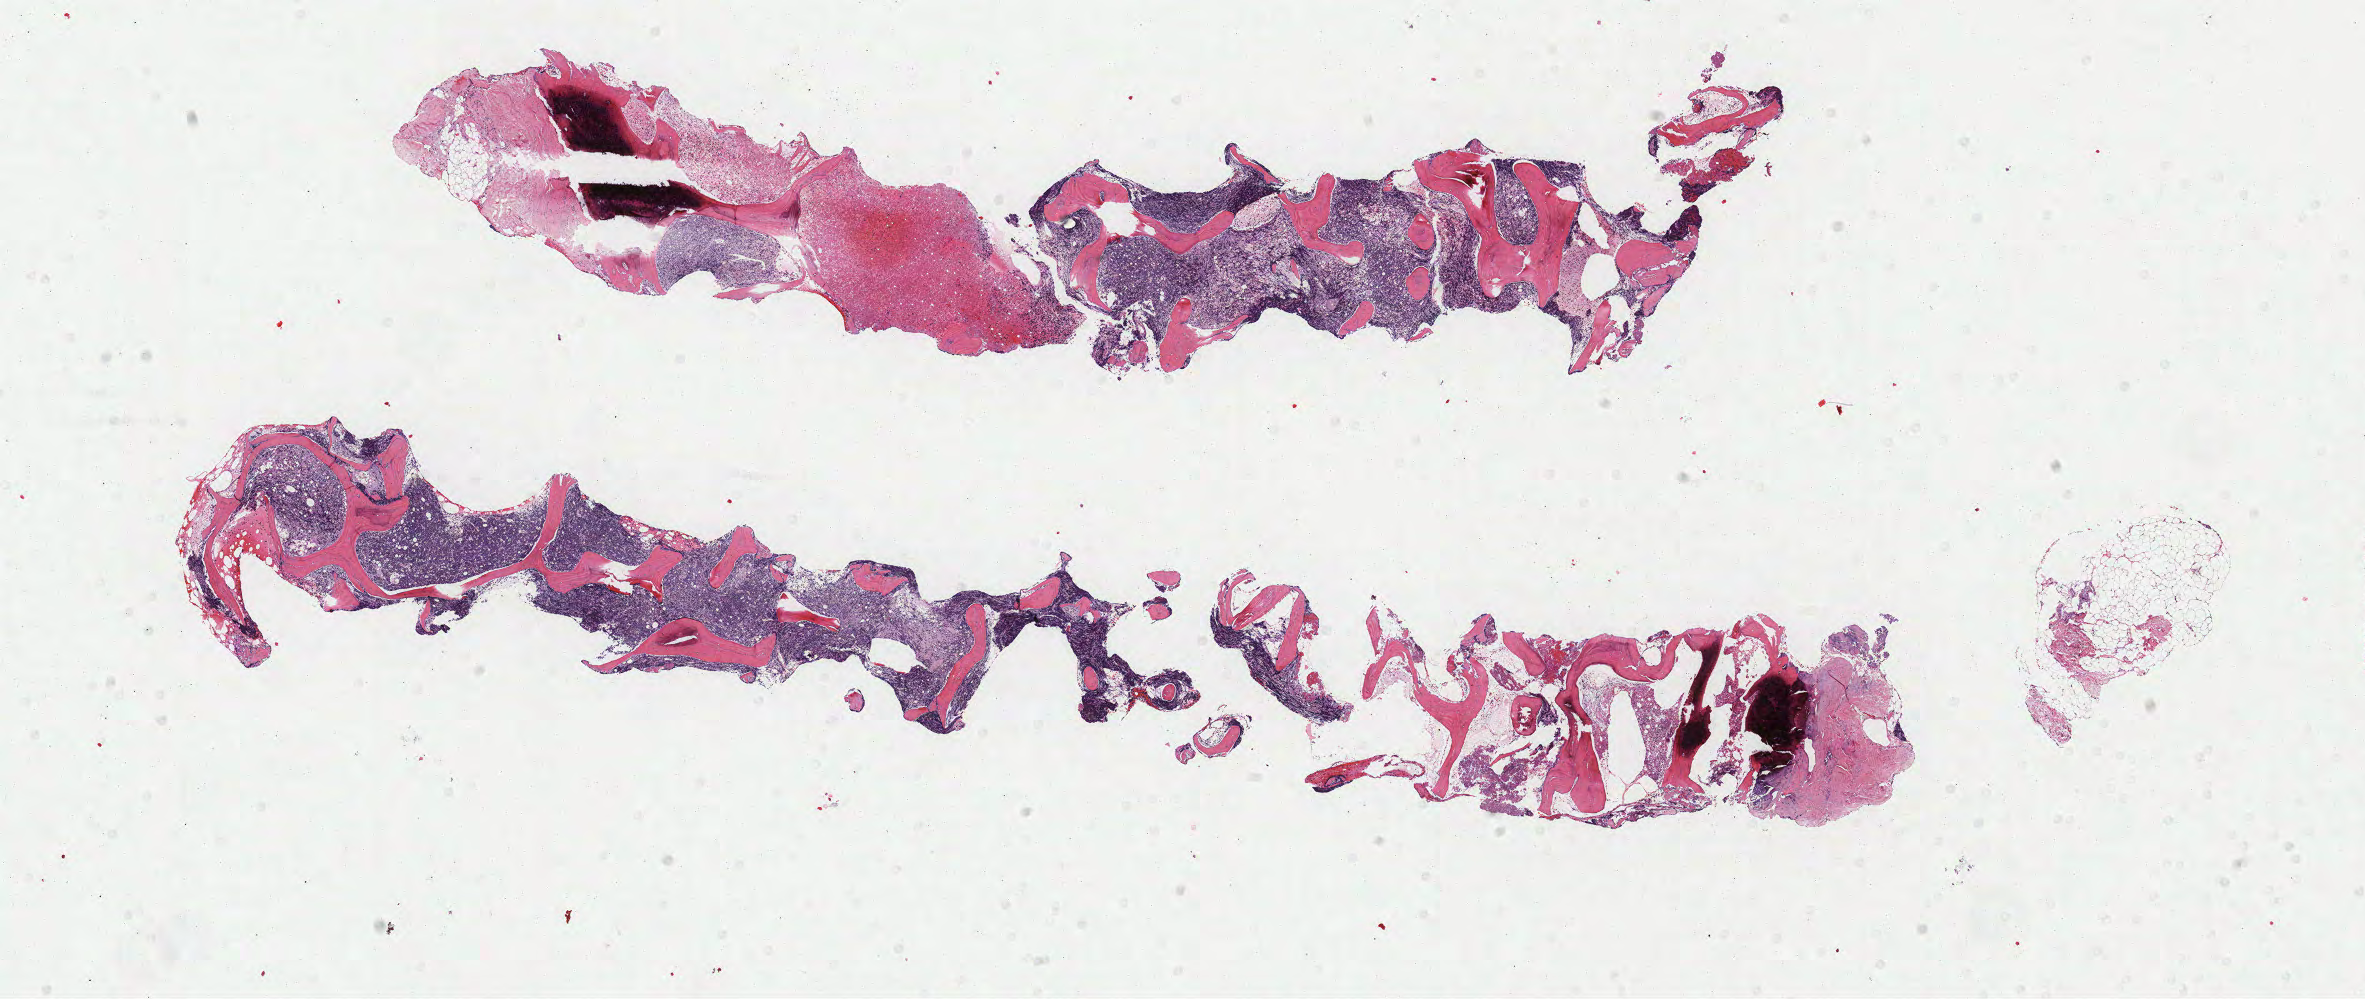
H&E whole-slide image — low-resolution overview of the scanned area, about 18.7 x 7.9 mm, FFPE section, primary tumor. Patient: female, aged 60. Slide review estimates, as recorded: tumor cells 50%, tumor nuclei 90%, stromal cells 30%, necrosis 10%, normal cells 10%. Infiltration values recorded for this section: lymphocyte infiltration 30%, monocyte infiltration 20%, neutrophil infiltration 10%.
Diagnosis: Burkitt lymphoma, NOS. Ann Arbor stage (patient): Stage IV.